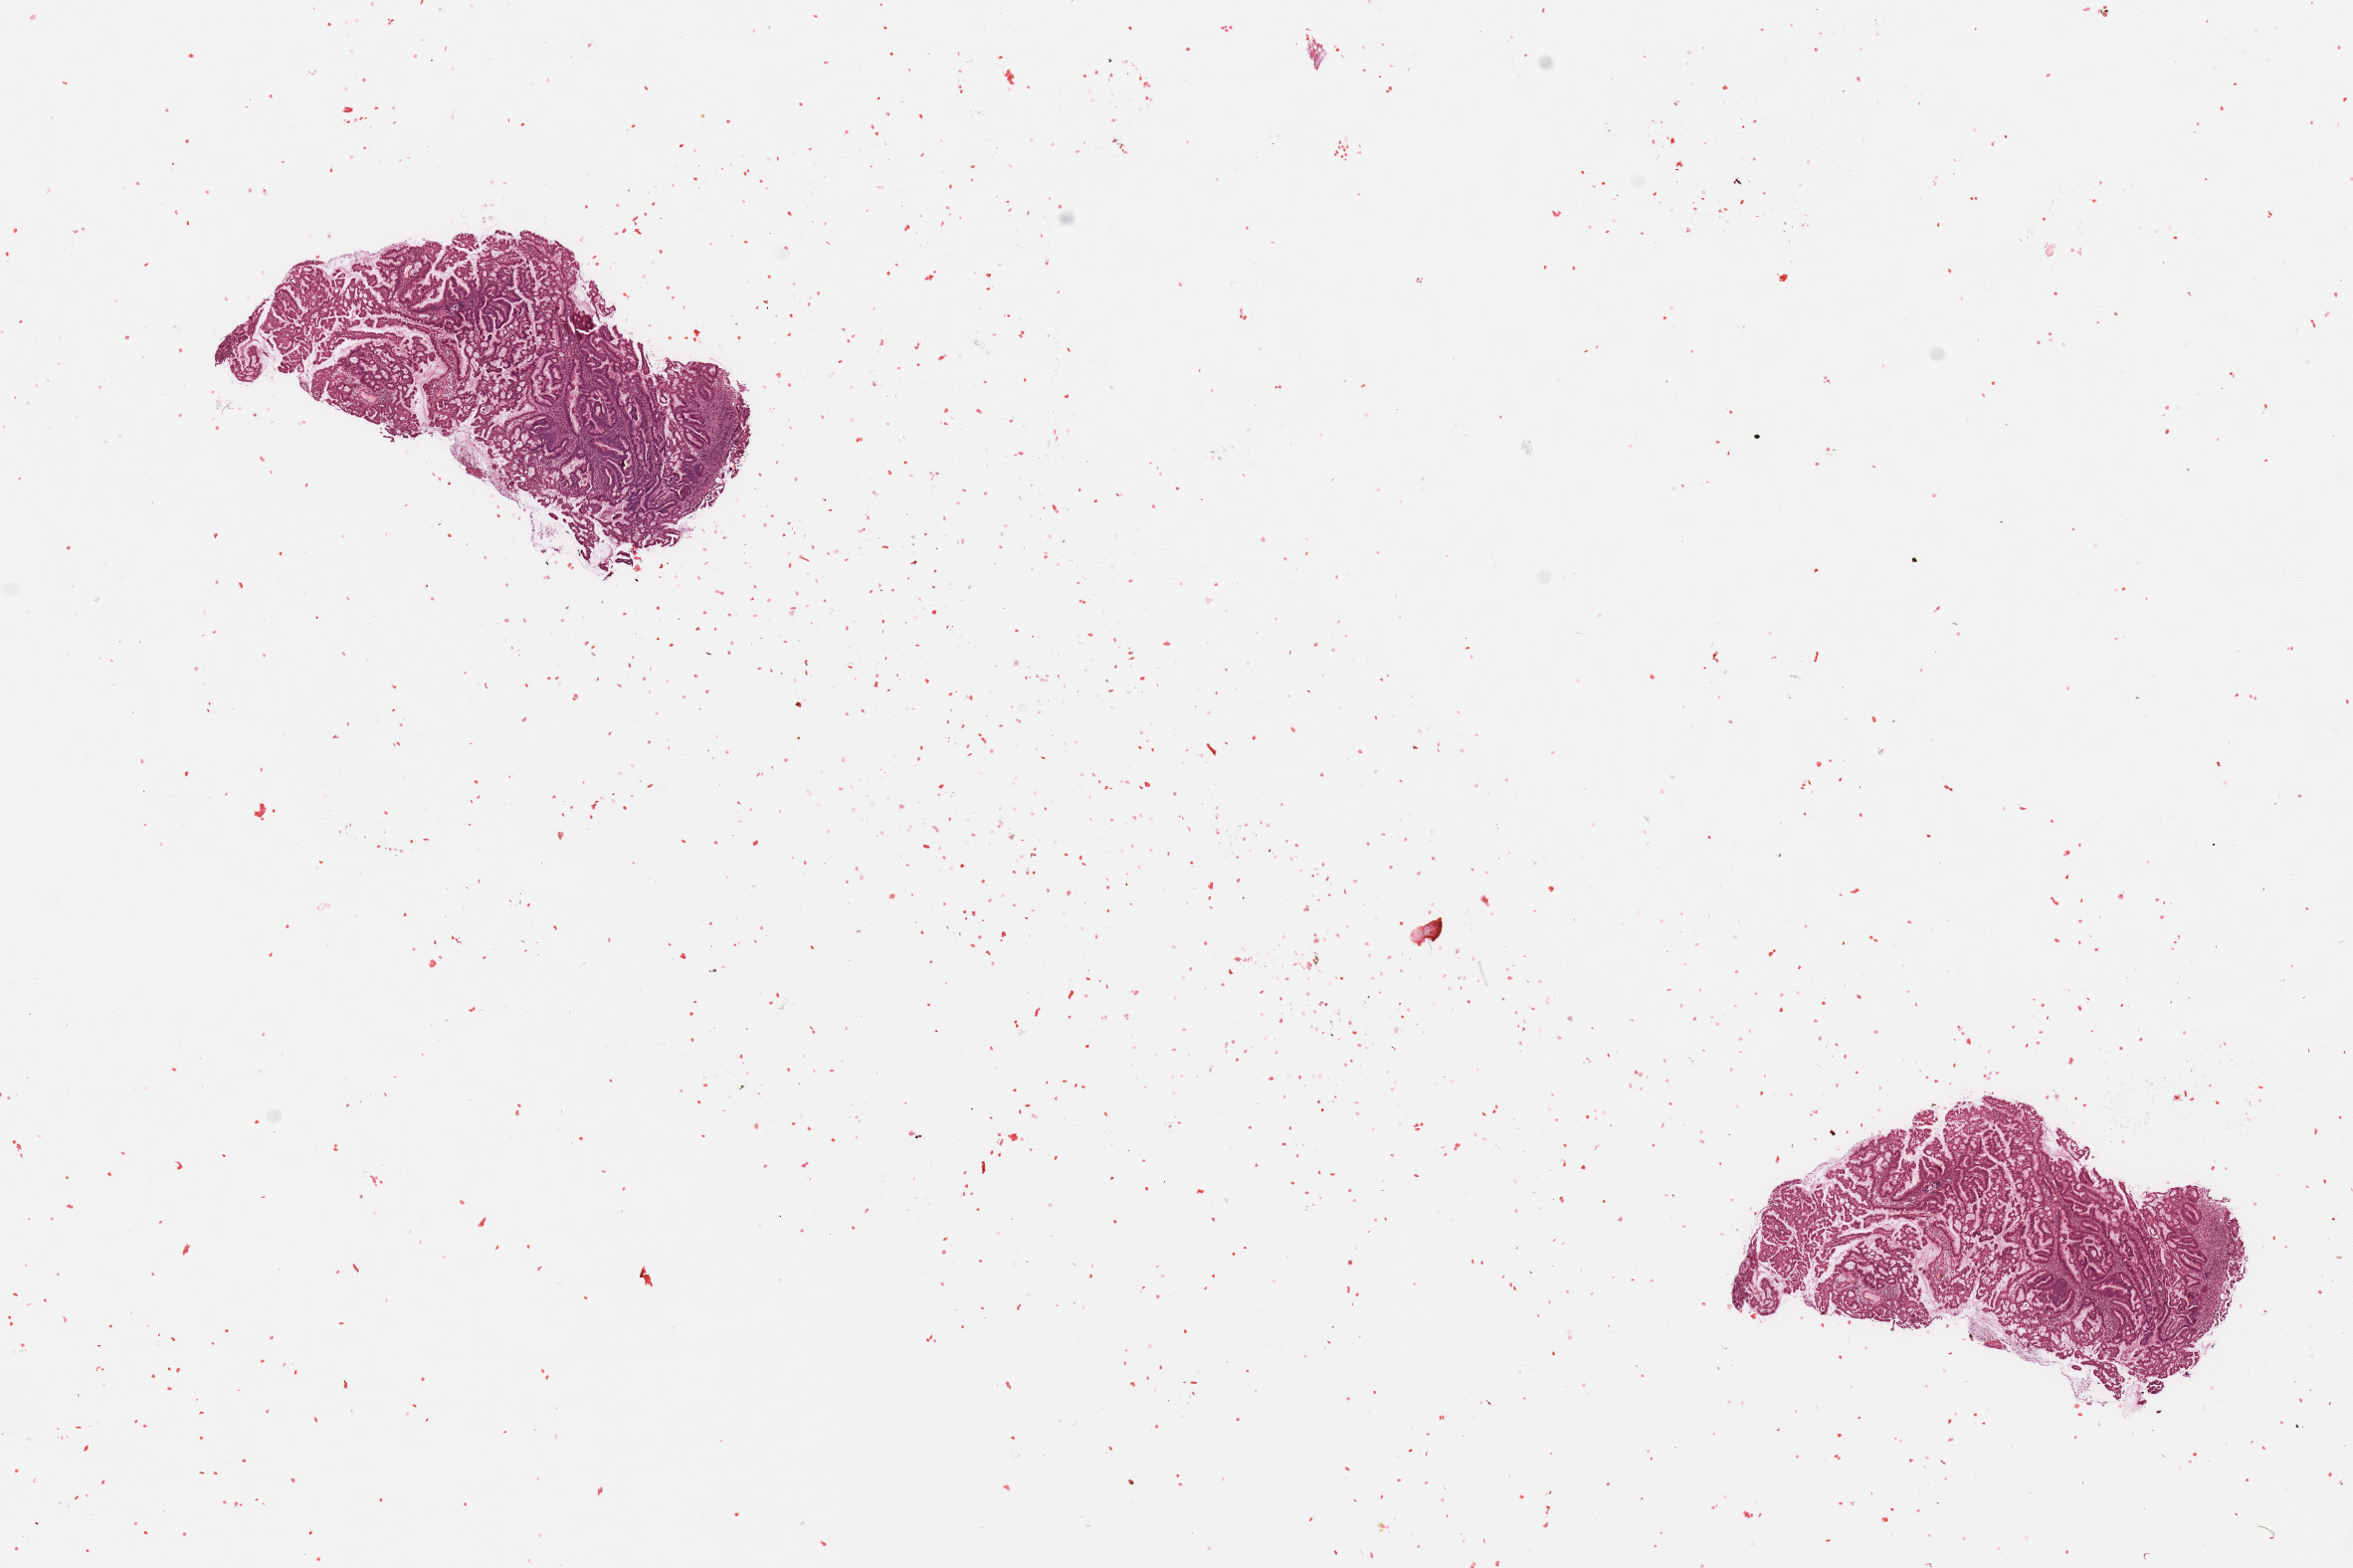
Hematoxylin and eosin (H&E) stained whole-slide image — a low-resolution overview of the entire scanned area, about 18.7 x 12.5 mm, uterus, tumour tissue. 83-year-old female patient. Histologic grade: G1 (well differentiated).
Primary tumour site (as recorded): posterior endometrium. AJCC pathologic stage: I. Diagnosis: Endometrioid adenocarcinoma, NOS.